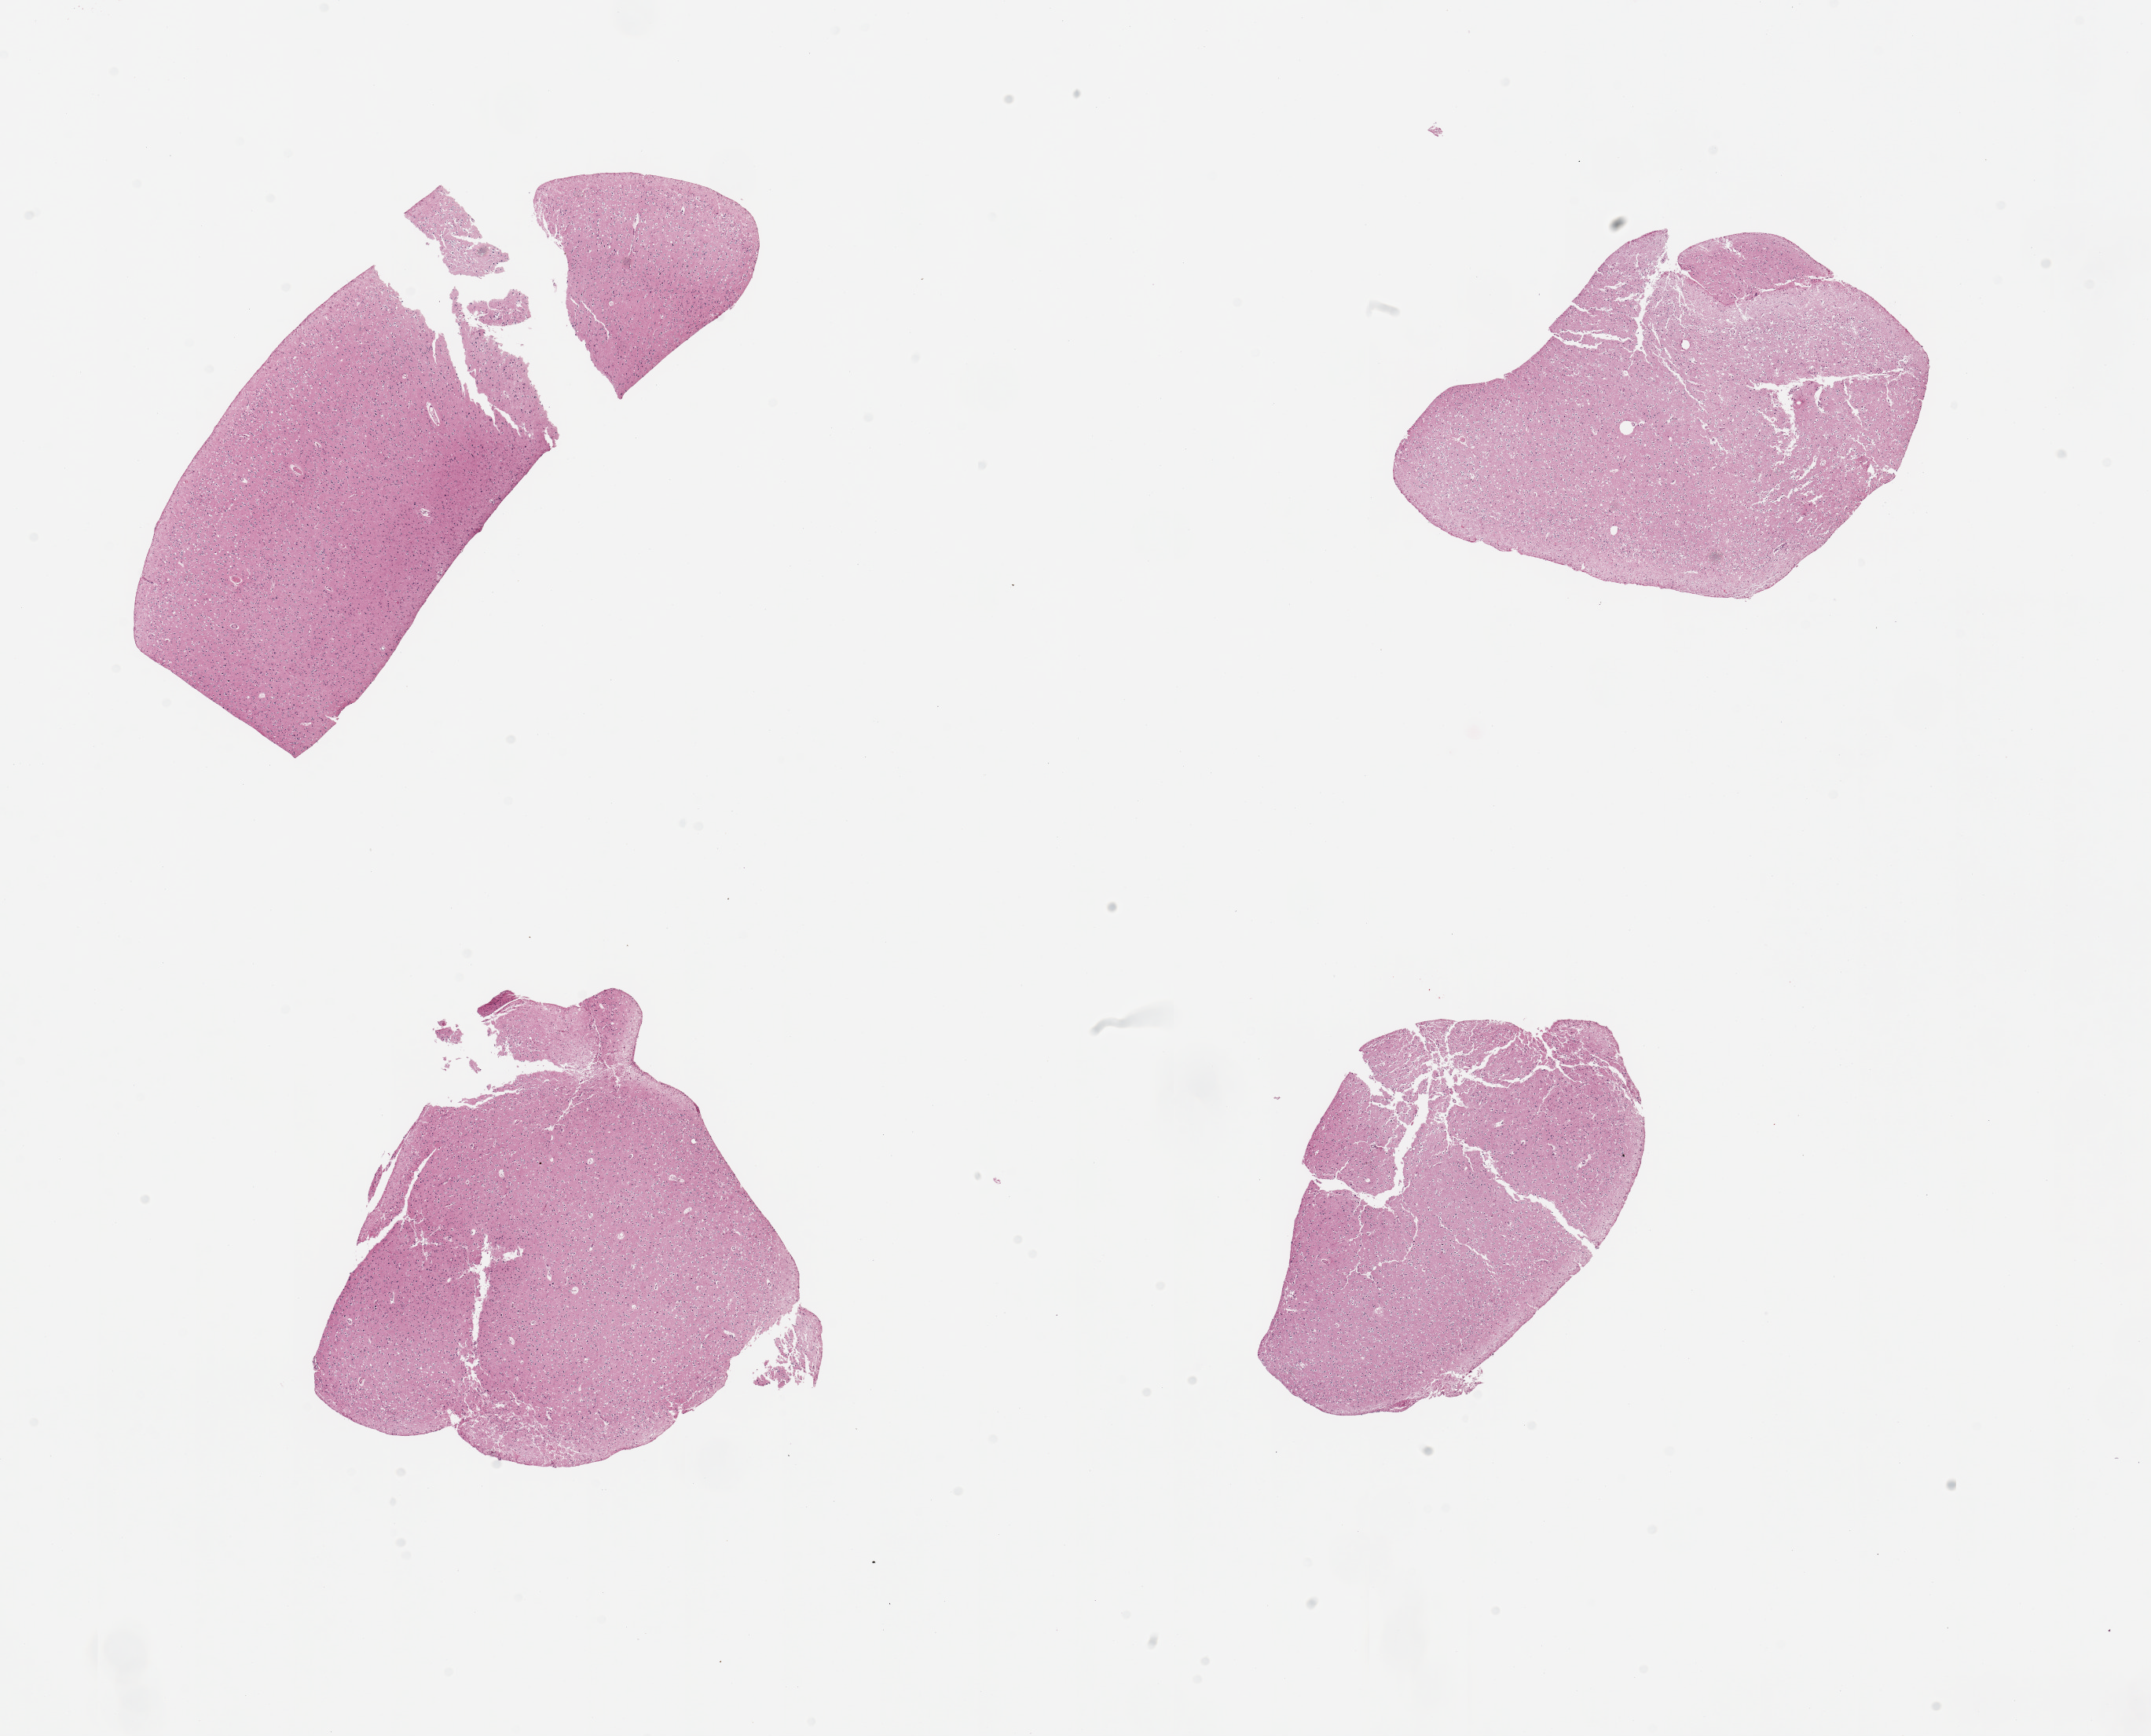
Digitized H&E-stained section, brightfield, a low-resolution overview of the entire scanned area, about 21.7 x 17.5 mm; PAXgene-fixed, paraffin-embedded tissue; sampled site (target tissue): cerebral cortex; donor tissue sample.
Pathologist's review note for this sample: 4 pieces, no abnormalities.